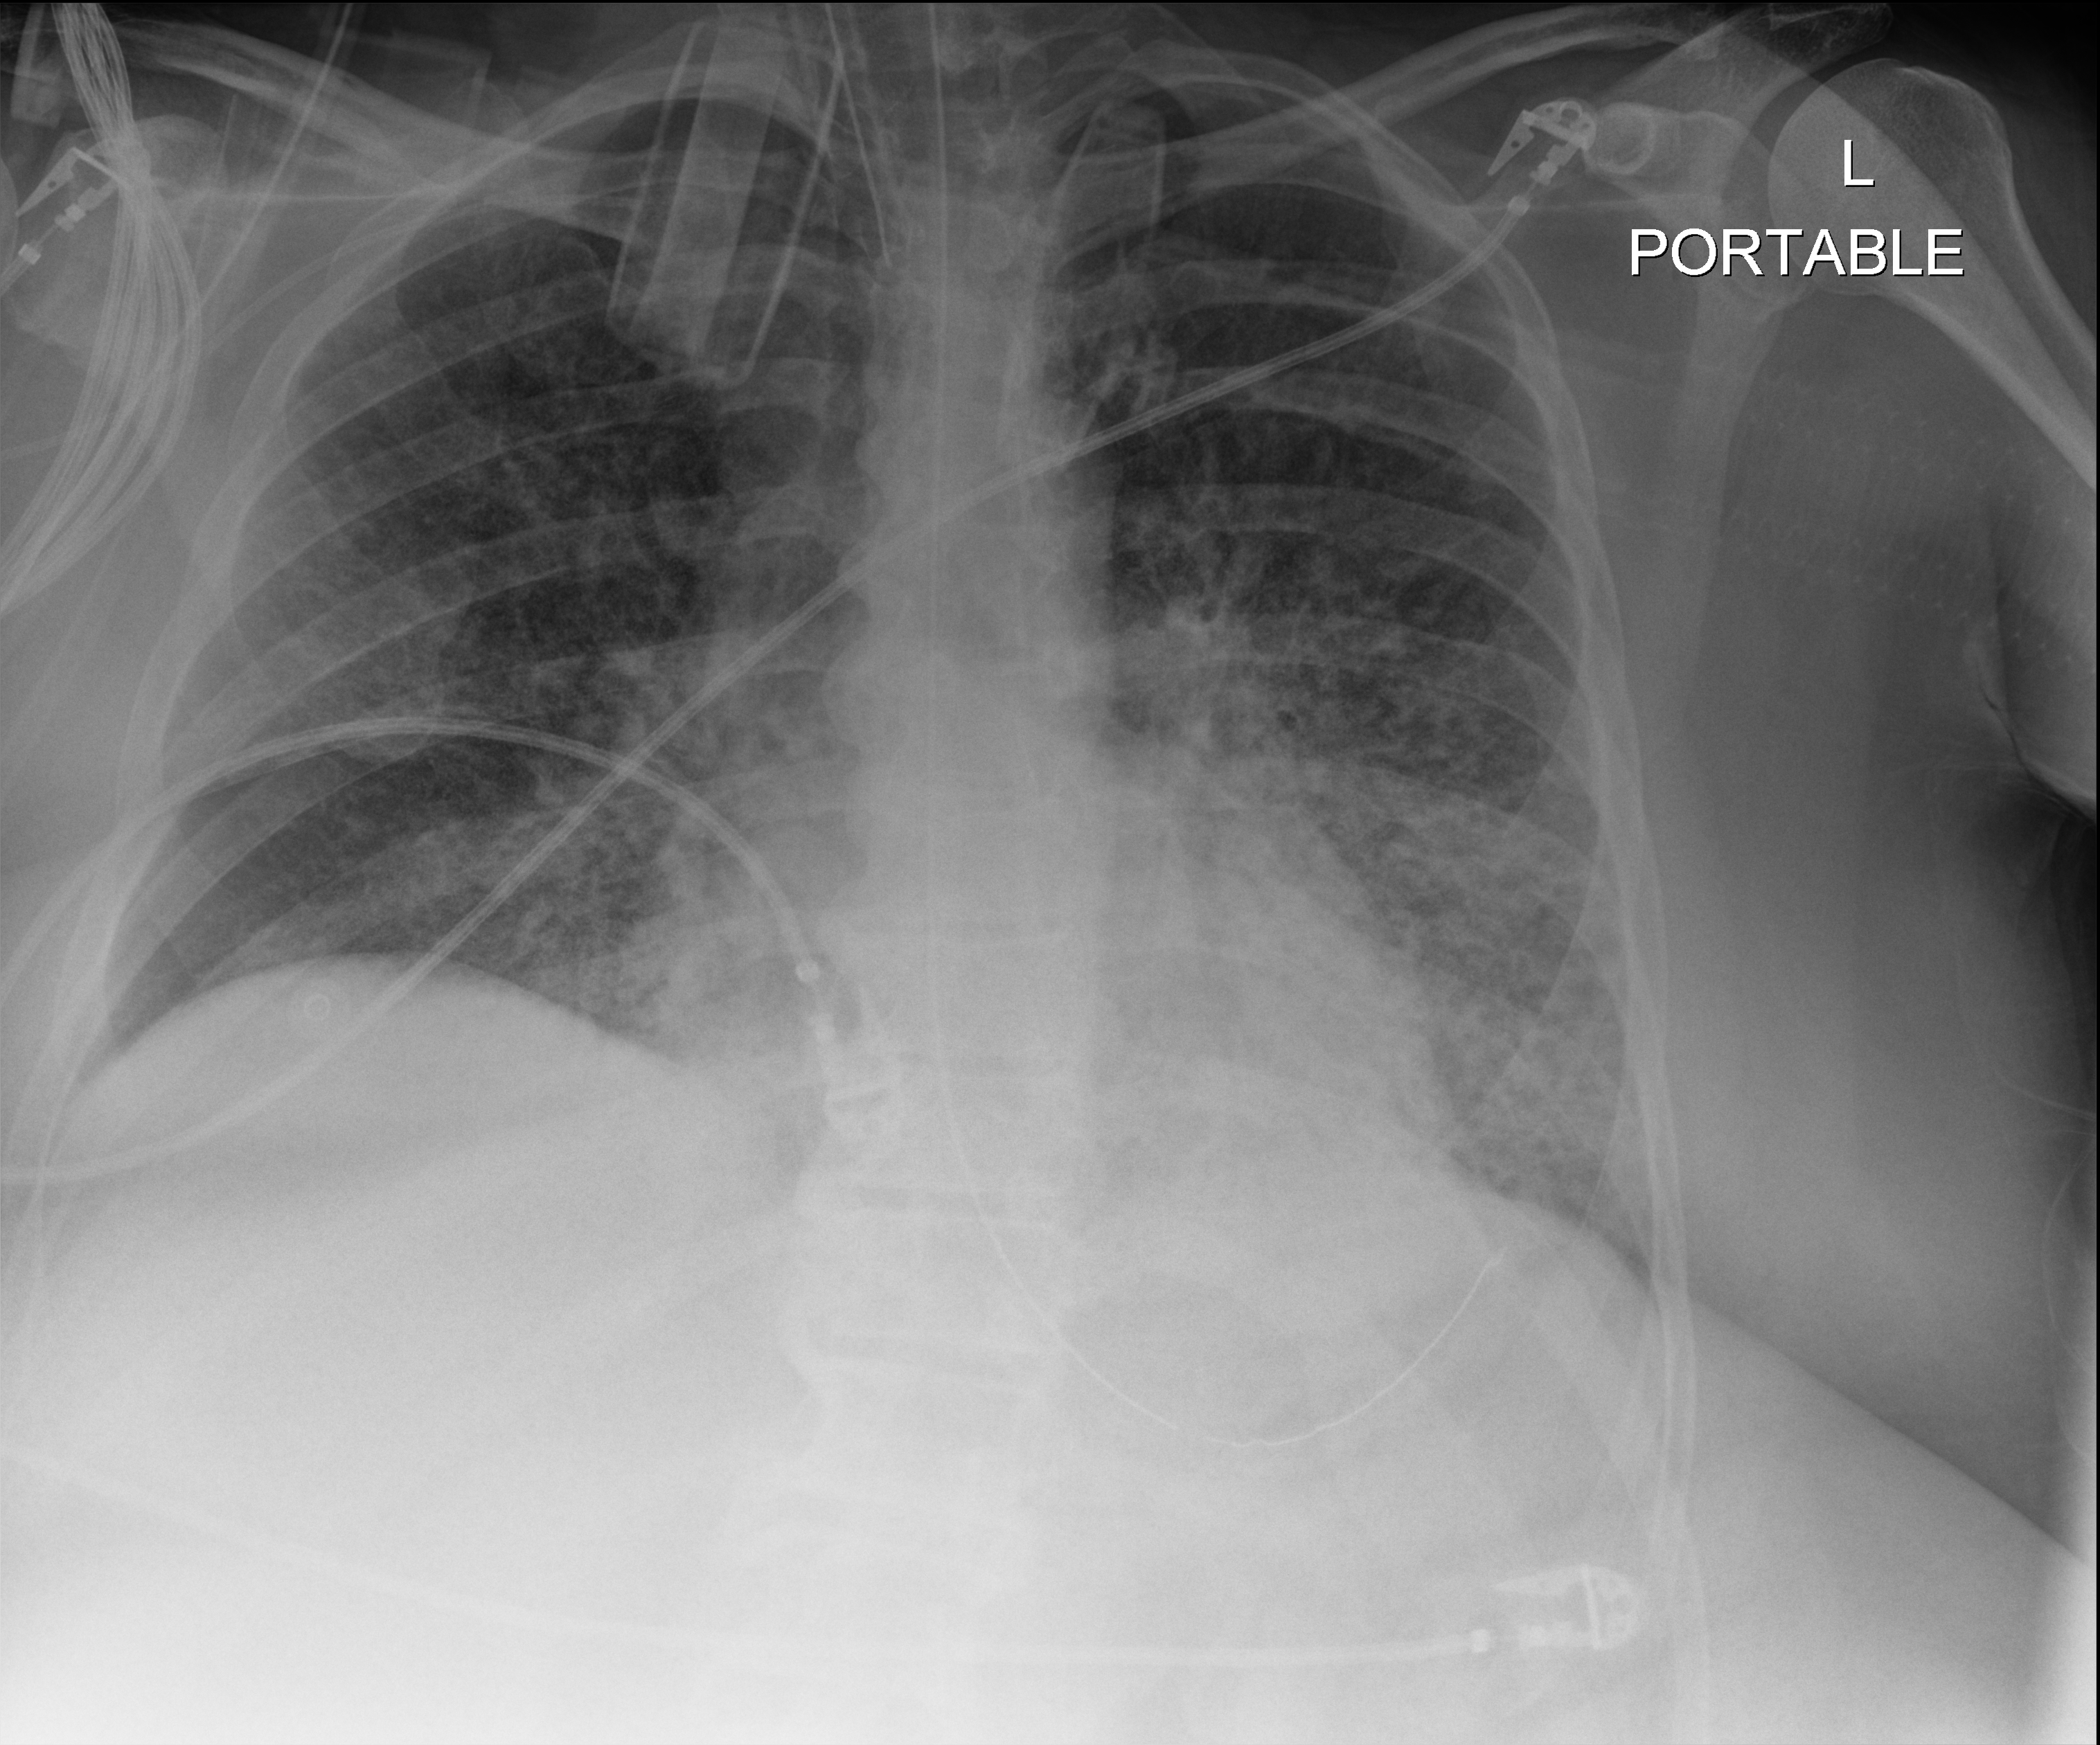
Chest radiograph (digital radiography), anteroposterior (AP) projection. Adult patient hospitalised with COVID-19, age 18–59 years.
From the hospital-stay record, not from the radiograph (when in the stay this image was taken is not recorded):
- length of hospital stay: 28 days